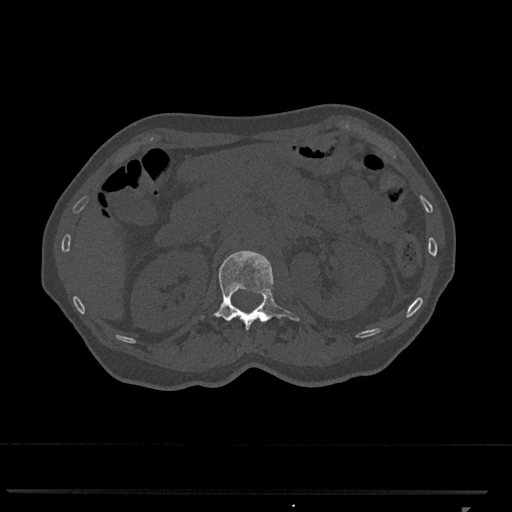
CT including the spine, one axial slice; position 404 of 793 along the scan axis; 120 kVp; bone window (W 1800 / L 400 HU); 0.5 mm slice thickness; 512 × 512 image matrix, field of view 380 × 380 mm. Female patient, age 62 years. Case-level facts recorded for this patient, not image findings: primary cancer: renal.
Annotated regions visible in this slice (semi-automatically segmented with operator editing):
- L1 vertebra: bounding box [x1, y1, x2, y2] px = [202, 250, 299, 330]